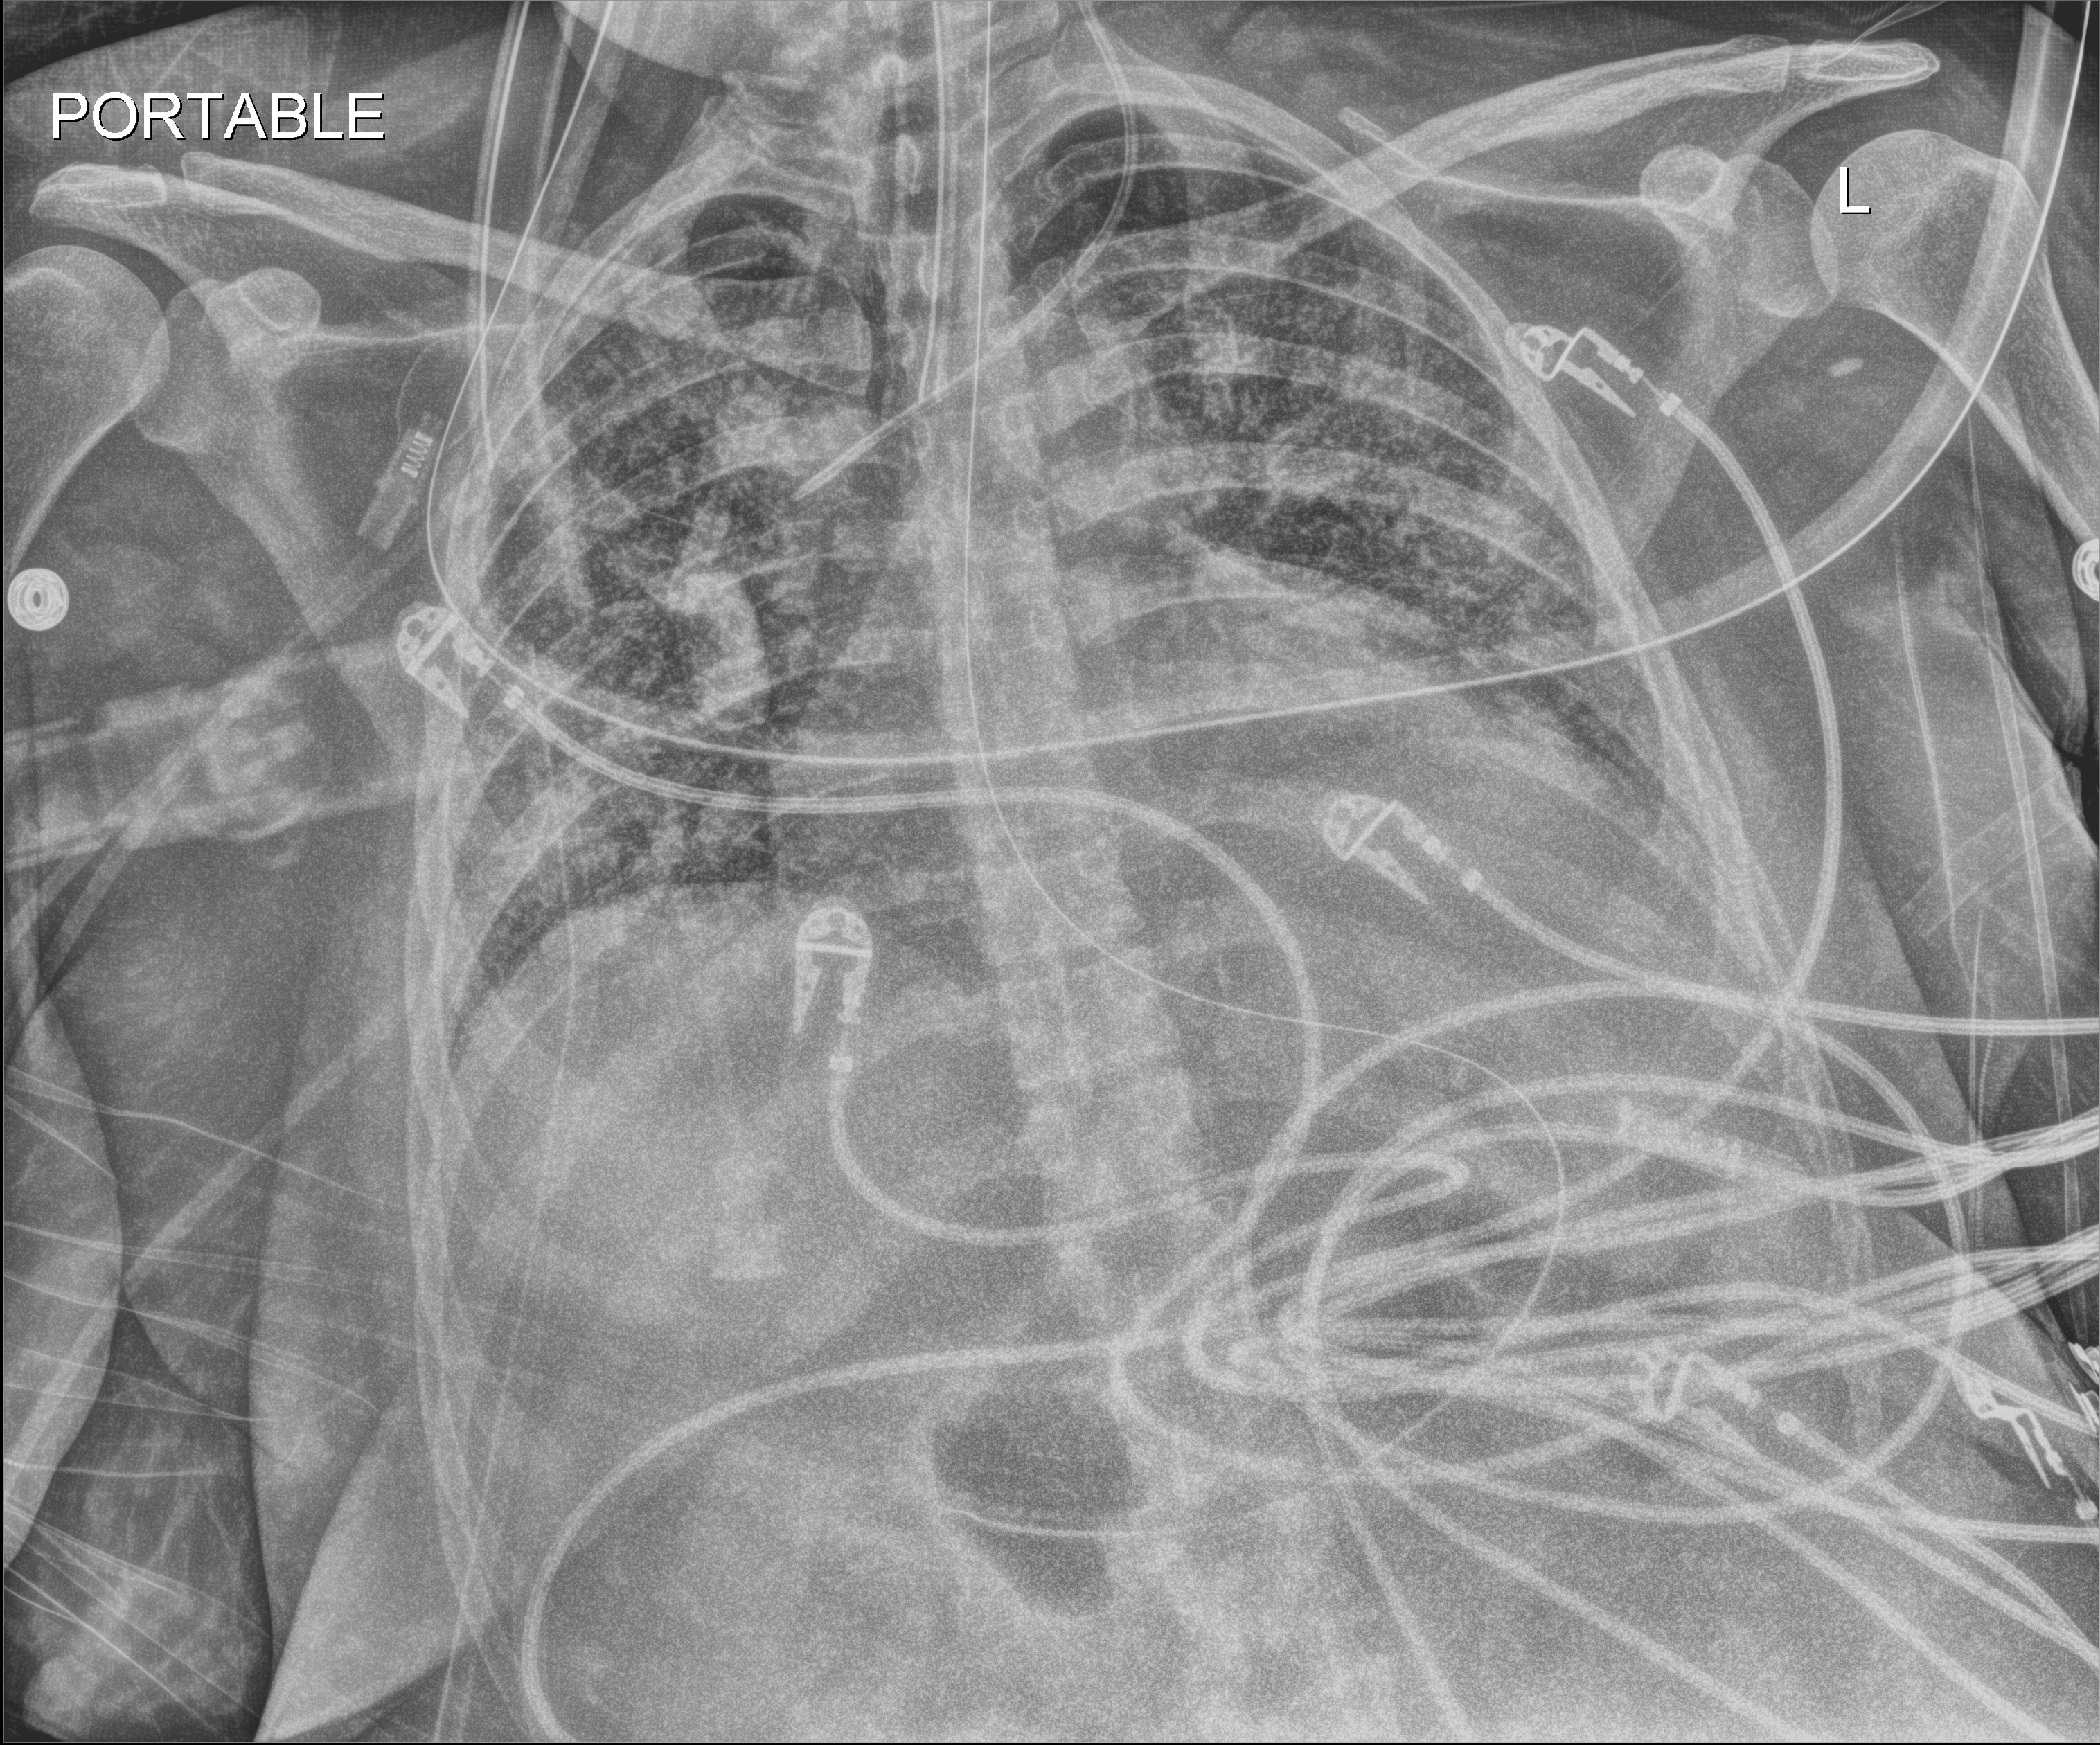
Chest X-ray (portable). Female patient hospitalised with COVID-19, age 18–59 years.
Admission-level facts for this patient (not findings on this image; timing relative to this image not recorded): admitted to intensive care during this hospital stay: no; mechanically ventilated during this hospital stay: yes.